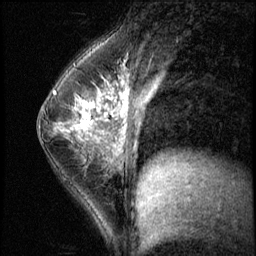
Breast MRI (dynamic contrast-enhanced), one sagittal slice. Slice 34 of 56 in the series (ordered by position). 3 images stored at this slice position (order not interpretable as contrast timing). 1.5 T. TE 4.2 ms, TR 8.7 ms. 2.5 mm slice thickness. 256 × 256 image matrix, field of view 180 × 180 mm. Female patient, age 35 years. Case-level facts recorded for this patient, not image findings: setting: breast cancer imaged before/during neoadjuvant chemotherapy; receptor status: HER2-positive.
Structures marked on this image (semi-automatically segmented with operator editing):
- analysis volume of interest (the breast-tissue region the enhancement analysis was run in; not a lesion): bounding box <58,84,138,186> (left, top, right, bottom; pixels)
- tumour enhancement mask (voxels above the 140 % enhancement threshold inside the analysis volume of interest): <58,84,107,139>